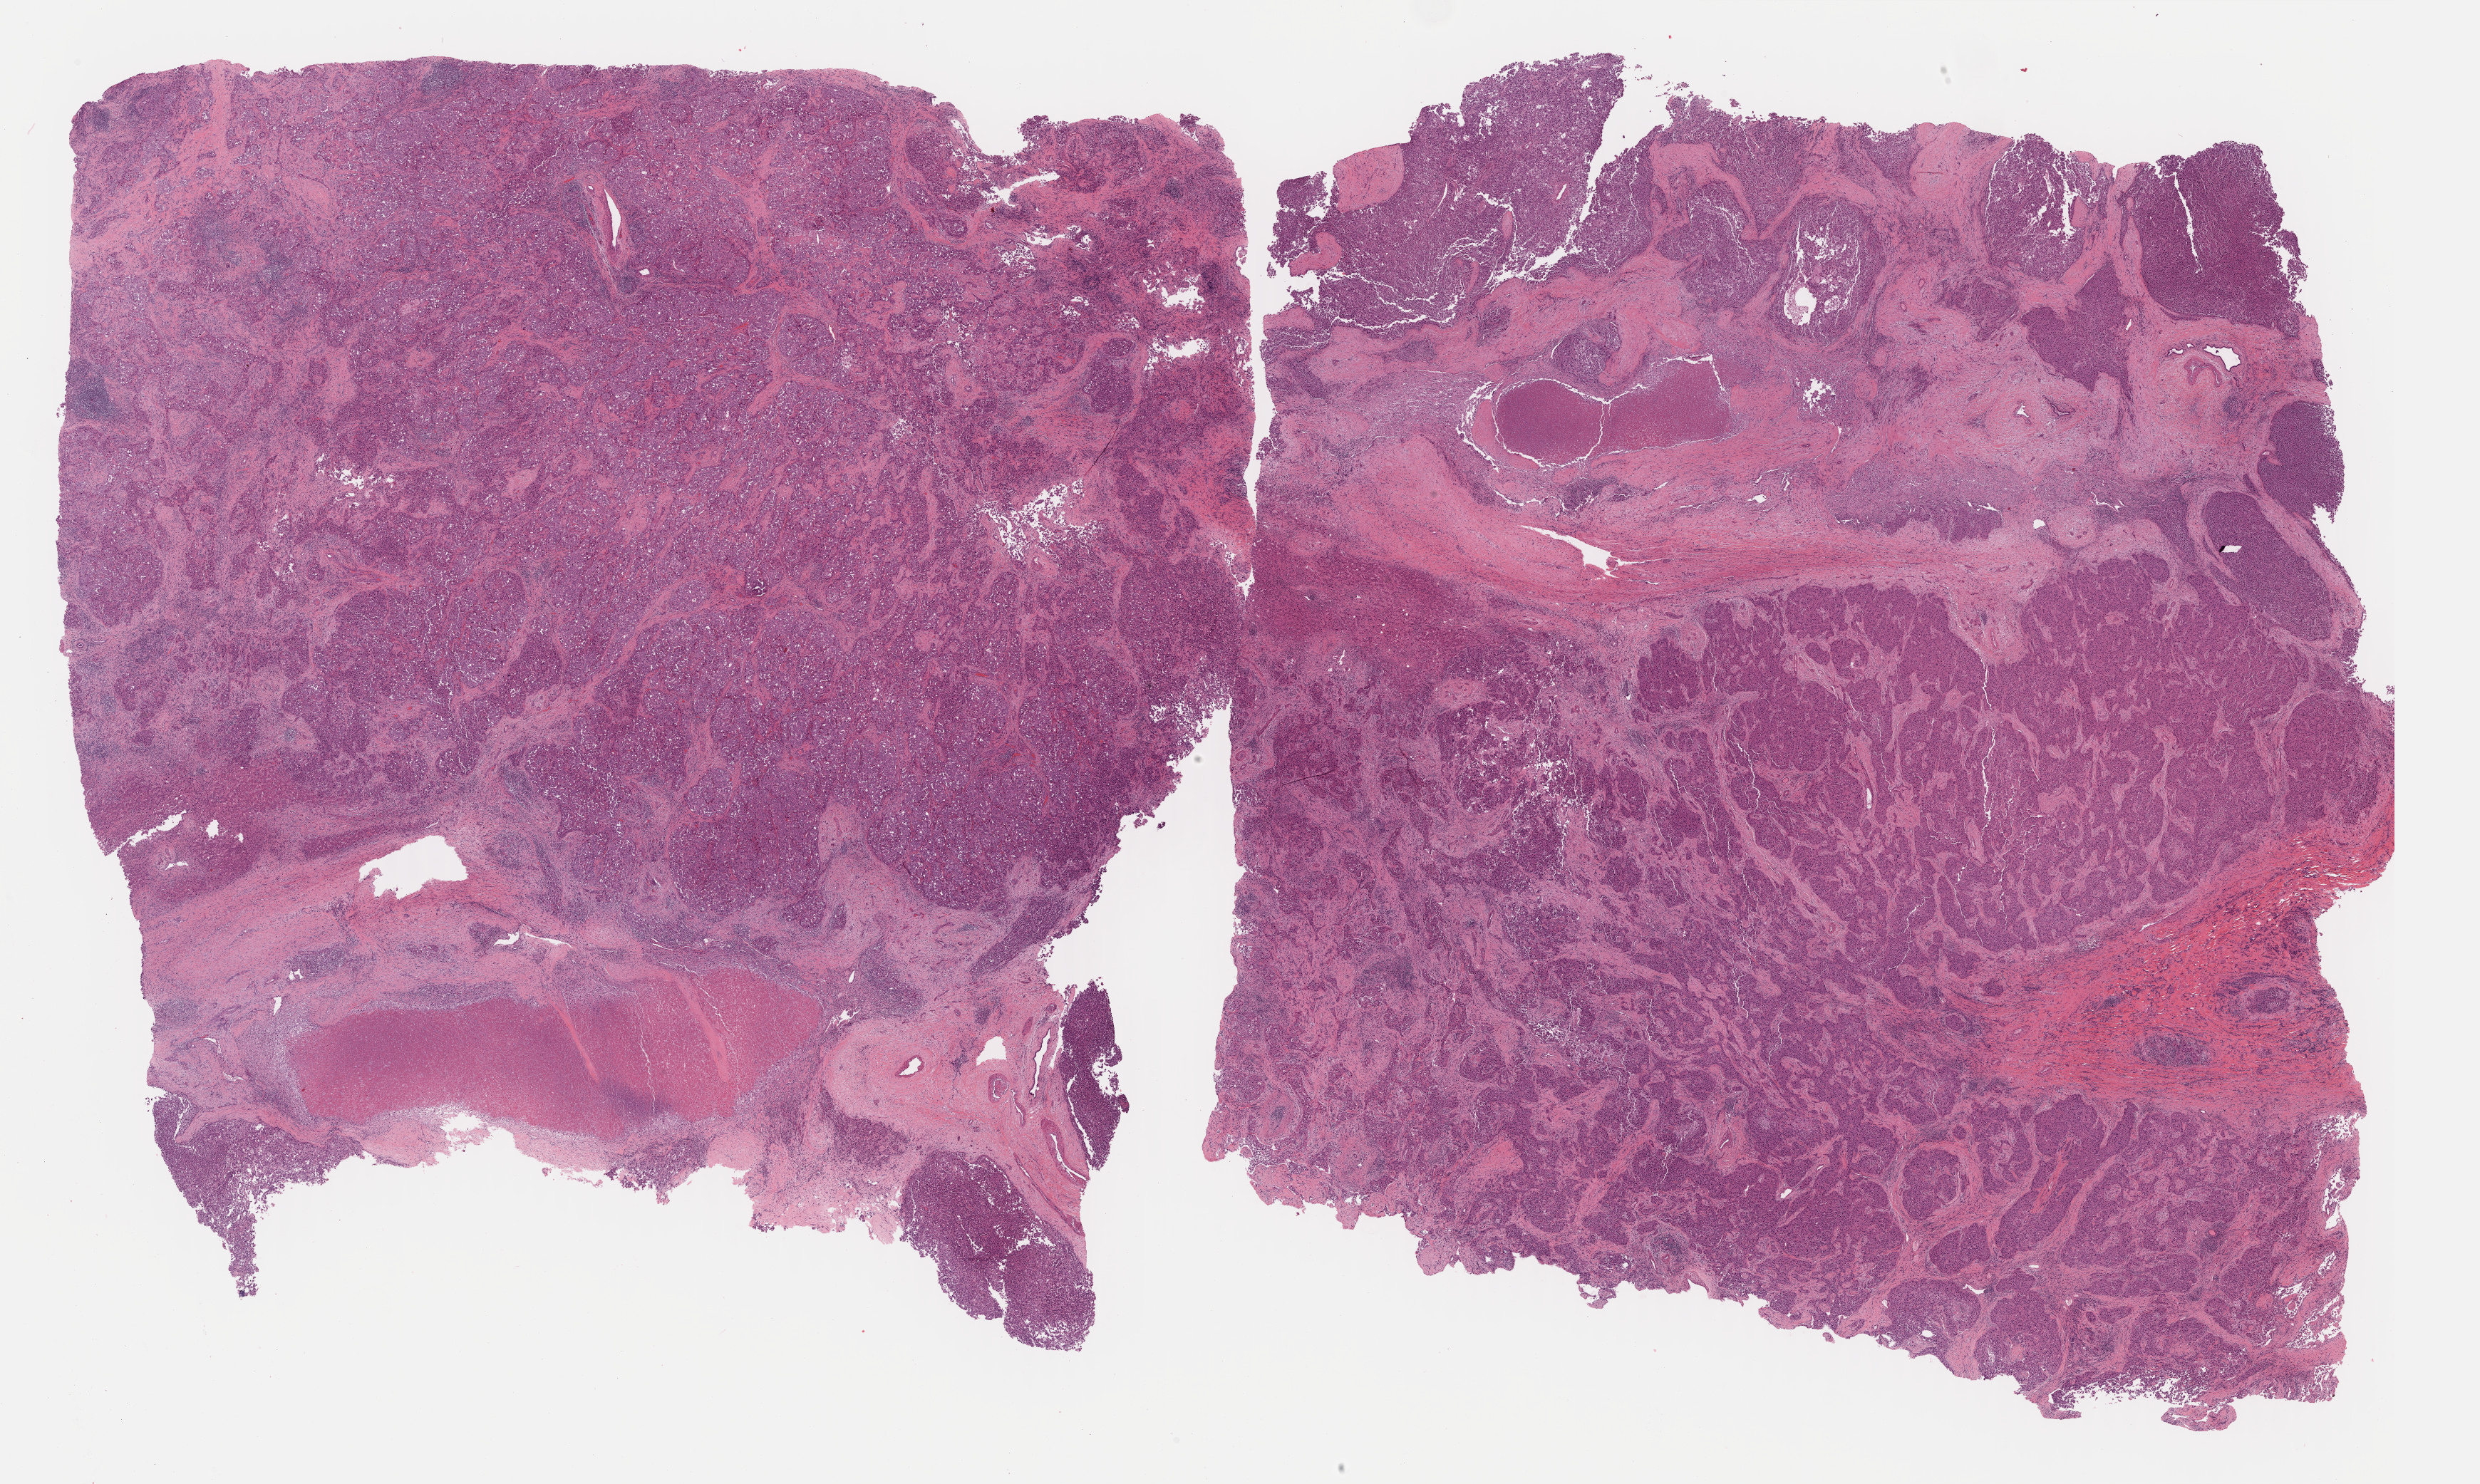
Whole-slide histology image, H&E-stained, shown as a low-resolution overview of the whole scanned area (about 28.2 x 16.9 mm). Formalin-fixed paraffin-embedded (FFPE) diagnostic section. Liver, primary tumour sample. Female, age 67 years at initial diagnosis. Histologic grade: G3 (poorly differentiated).
AJCC pathologic stage: IIIC. Diagnosis: Hepatocellular carcinoma, NOS.